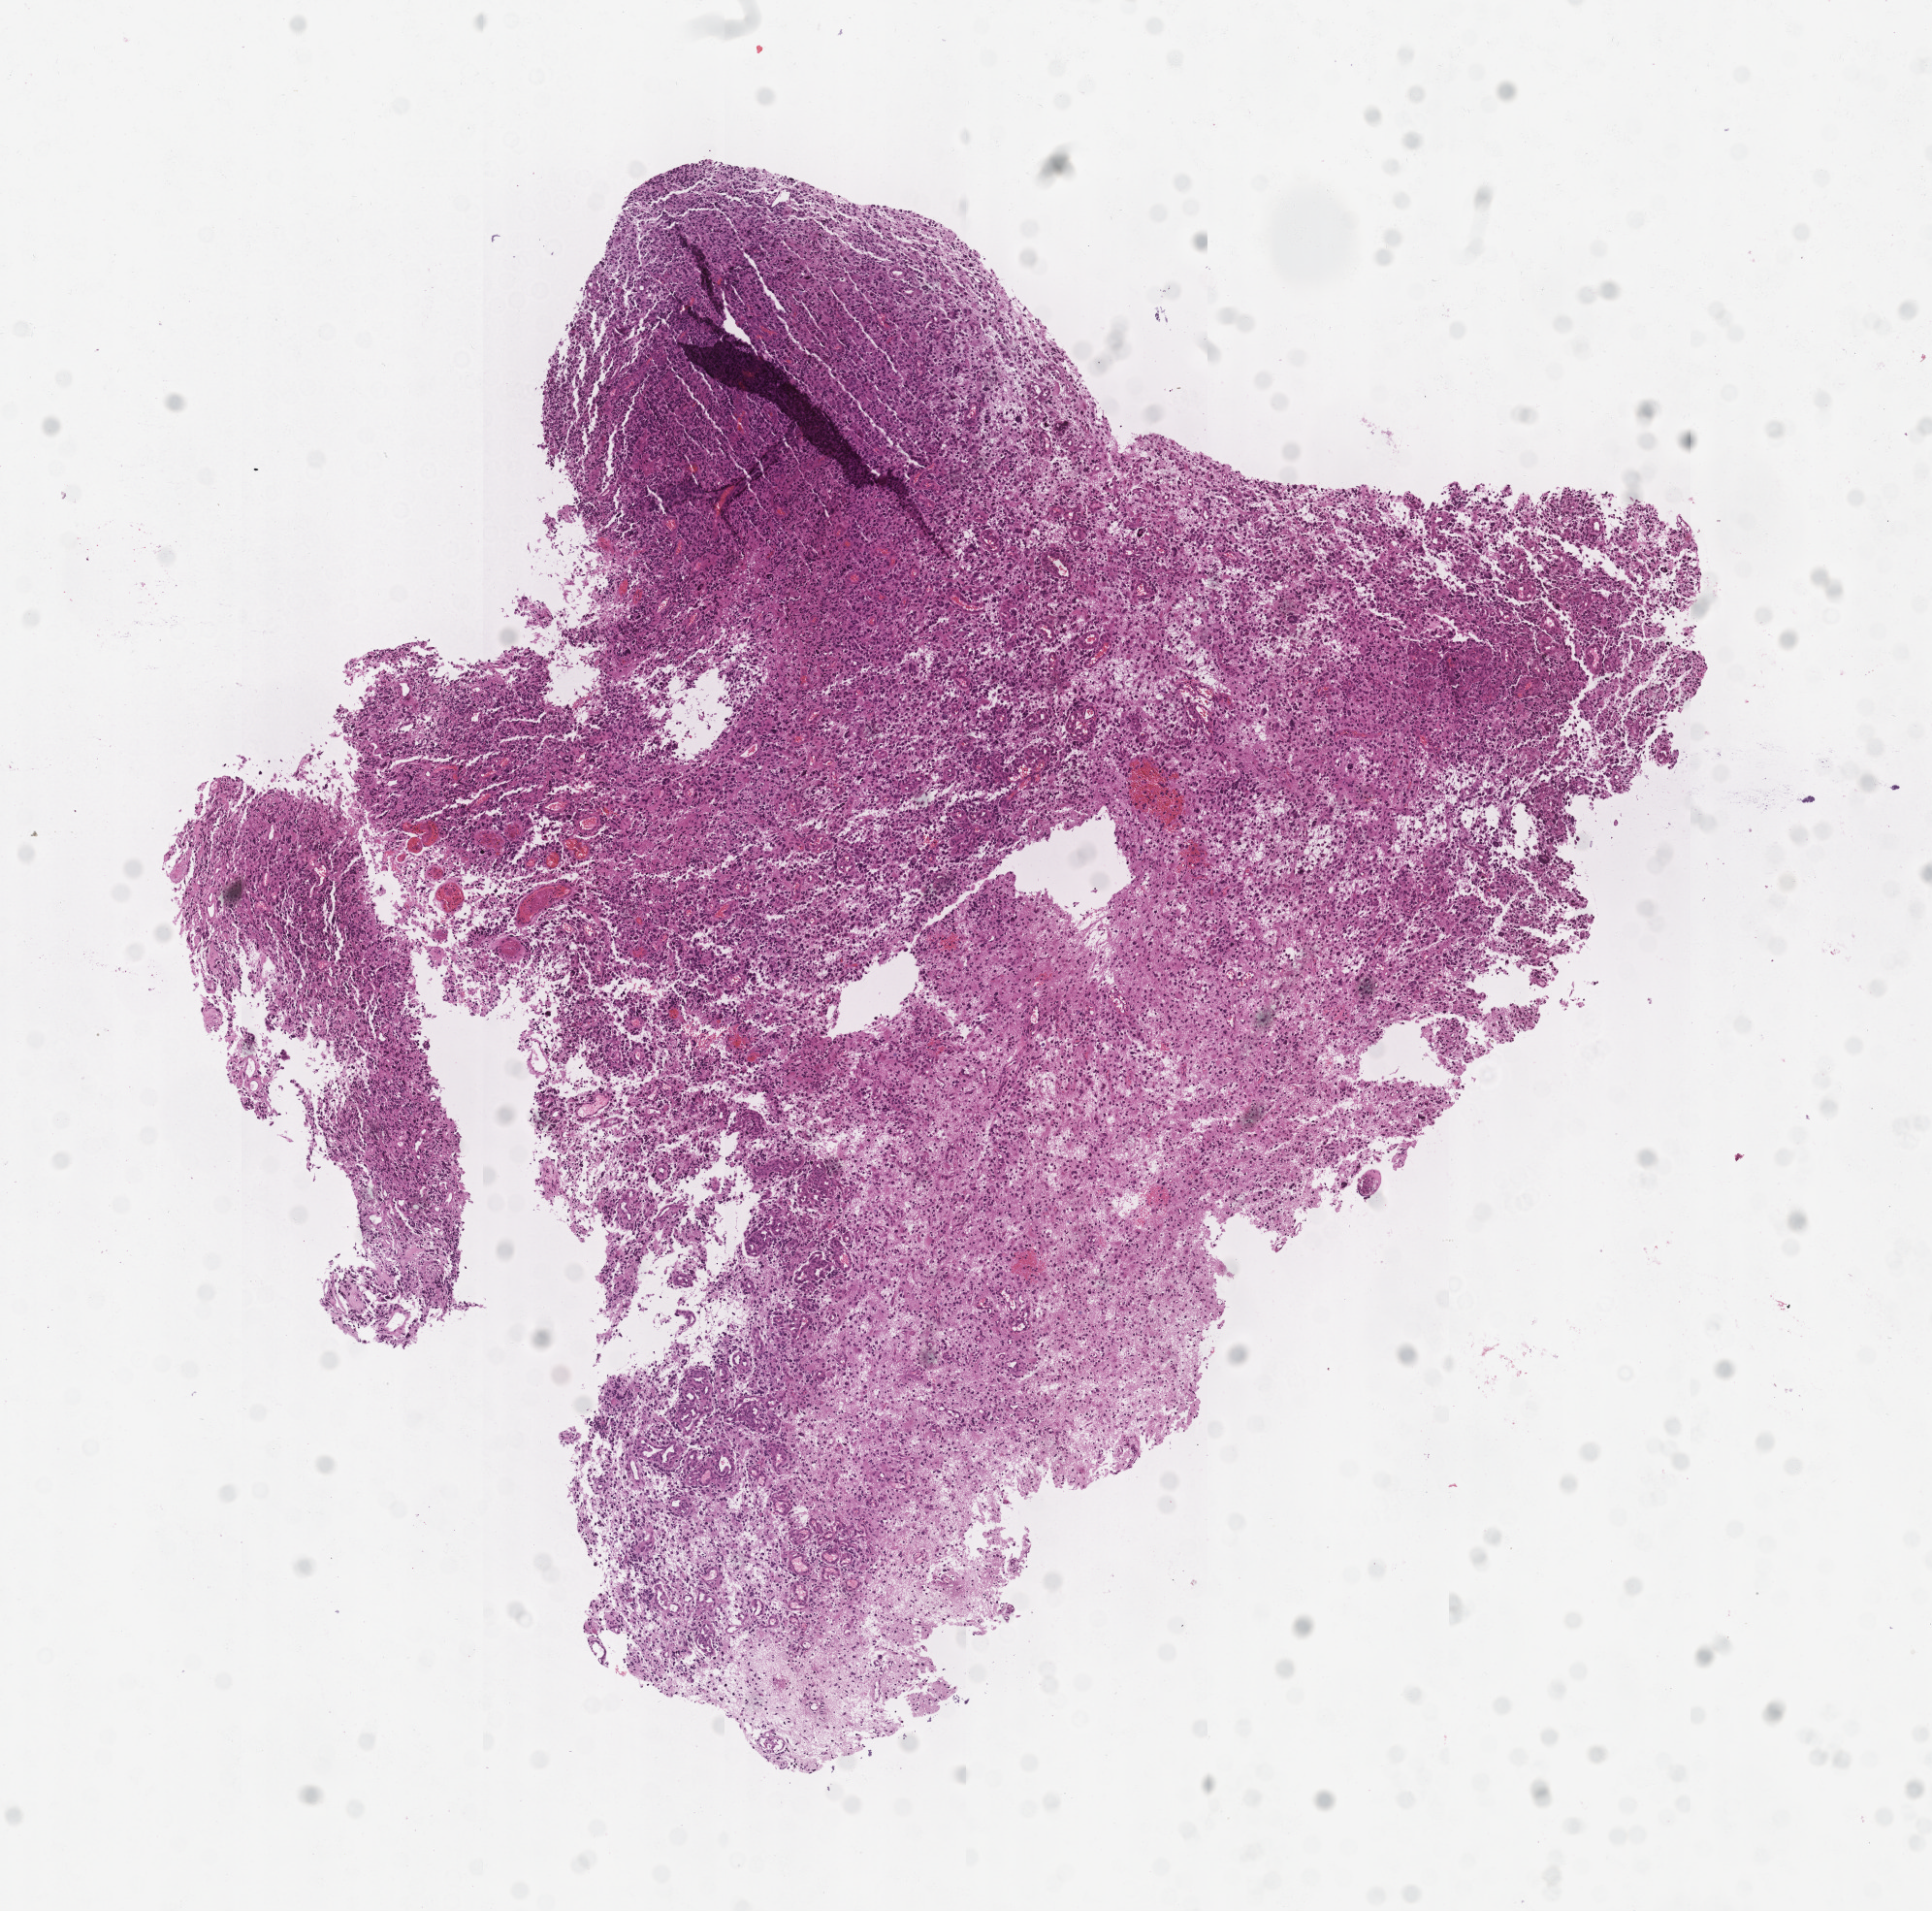
H&E whole-slide image, whole scanned area (about 8.0 x 7.9 mm, acquisition: 20x scan) shown as a low-resolution overview, tumour tissue sample, brain. Male, 65 y/o.
Primary tumour site (as recorded): temporal lobe. Diagnosis: Glioblastoma.